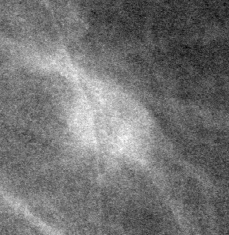
Crop from a digitized film mammogram around one marked abnormality; left breast; CC view; BI-RADS breast density category 1 (scale 1–4).
Finding: mass, shape oval, margins circumscribed; BI-RADS assessment category 4; subtlety rating 3 on a 1 (subtle) to 5 (obvious) scale; pathology result (as recorded, not read from the image): malignant.